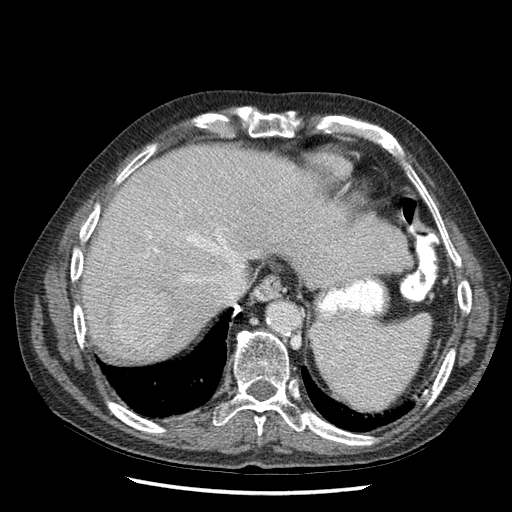
Contrast-enhanced abdominal CT (liver protocol), one axial slice. Slice 50 of 67 in the series (ordered by position). Reconstruction kernel STANDARD. Soft-tissue window (W 400 / L 40 HU). 2.5 mm slice thickness. 512 × 512 image matrix. Case-level facts recorded for this patient, not image findings: diagnosis: hepatocellular carcinoma (patient treated with transarterial chemoembolisation; whether this scan precedes or follows treatment is not stated here); TNM stage (as recorded): Stage-I; Child-Pugh class: A; tumour differentiation: moderately differentiated; tumour nodularity: uninodular.
Structures marked on this image (semi-automatically segmented with operator editing):
- liver parenchyma outside the tumour (the mass and vessels are separate outlines, so this box may not span the whole liver): bounding box <76,141,412,366> (left, top, right, bottom; pixels)
- mass: <112,288,173,347>
- liver vessels: <145,200,246,301>